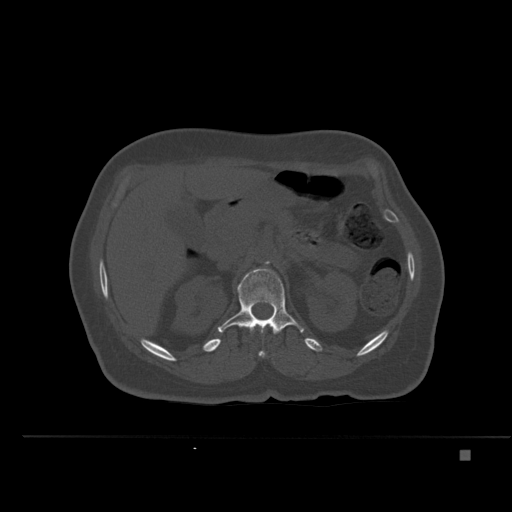
CT including the spine, one axial slice; bone window (W 1800 / L 400 HU); 512 × 512 image matrix, field of view 422 × 422 mm. Female patient, age 74 years. Case-level facts recorded for this patient, not image findings: primary cancer: colon.
Outlined on this slice (semi-automatically segmented with operator editing):
- L1 vertebra: bounding box [x1, y1, x2, y2] px = [218, 269, 304, 334]
- T12 vertebra: [251, 325, 278, 357]